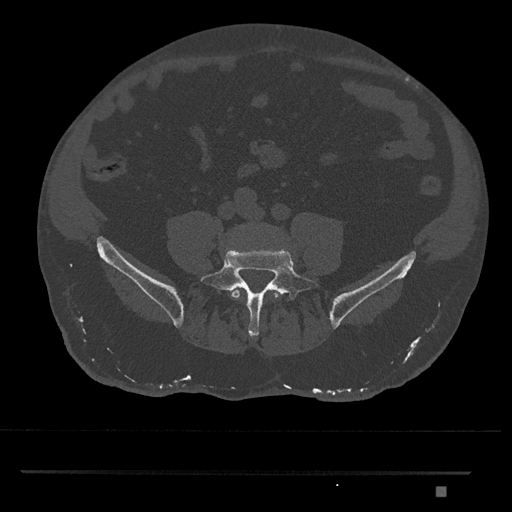
CT including the spine, one axial slice. Reconstruction kernel Br40s/3. 120 kVp. Bone window (W 1800 / L 400 HU). 512 × 512 image matrix. Patient: male, 65 years. From the clinical record (not read from this slice): primary cancer: prostate.
Annotated regions visible in this slice (semi-automatically segmented with operator editing):
- L4 vertebra: bounding box <230,287,281,300> (left, top, right, bottom; pixels)
- L5 vertebra: <200,247,320,338>